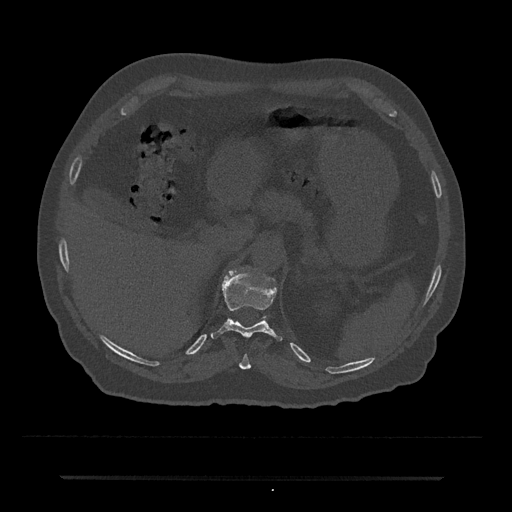
CT including the spine, one axial slice; slice 179 of 797 in the series (ordered by position); reconstruction kernel Br40s/3; 120 kVp; bone window (W 1800 / L 400 HU); 512 × 512 image matrix, field of view 437 × 437 mm. Male patient, age 69 years. From the clinical record (not read from this slice): primary cancer: prostate.
Structures marked on this image (semi-automatic segmentation, software-assisted and operator-edited):
- T10 vertebra: bounding box (x1, y1, x2, y2) in pixels: (239, 354, 251, 370)
- T11 vertebra: (211, 272, 283, 341)